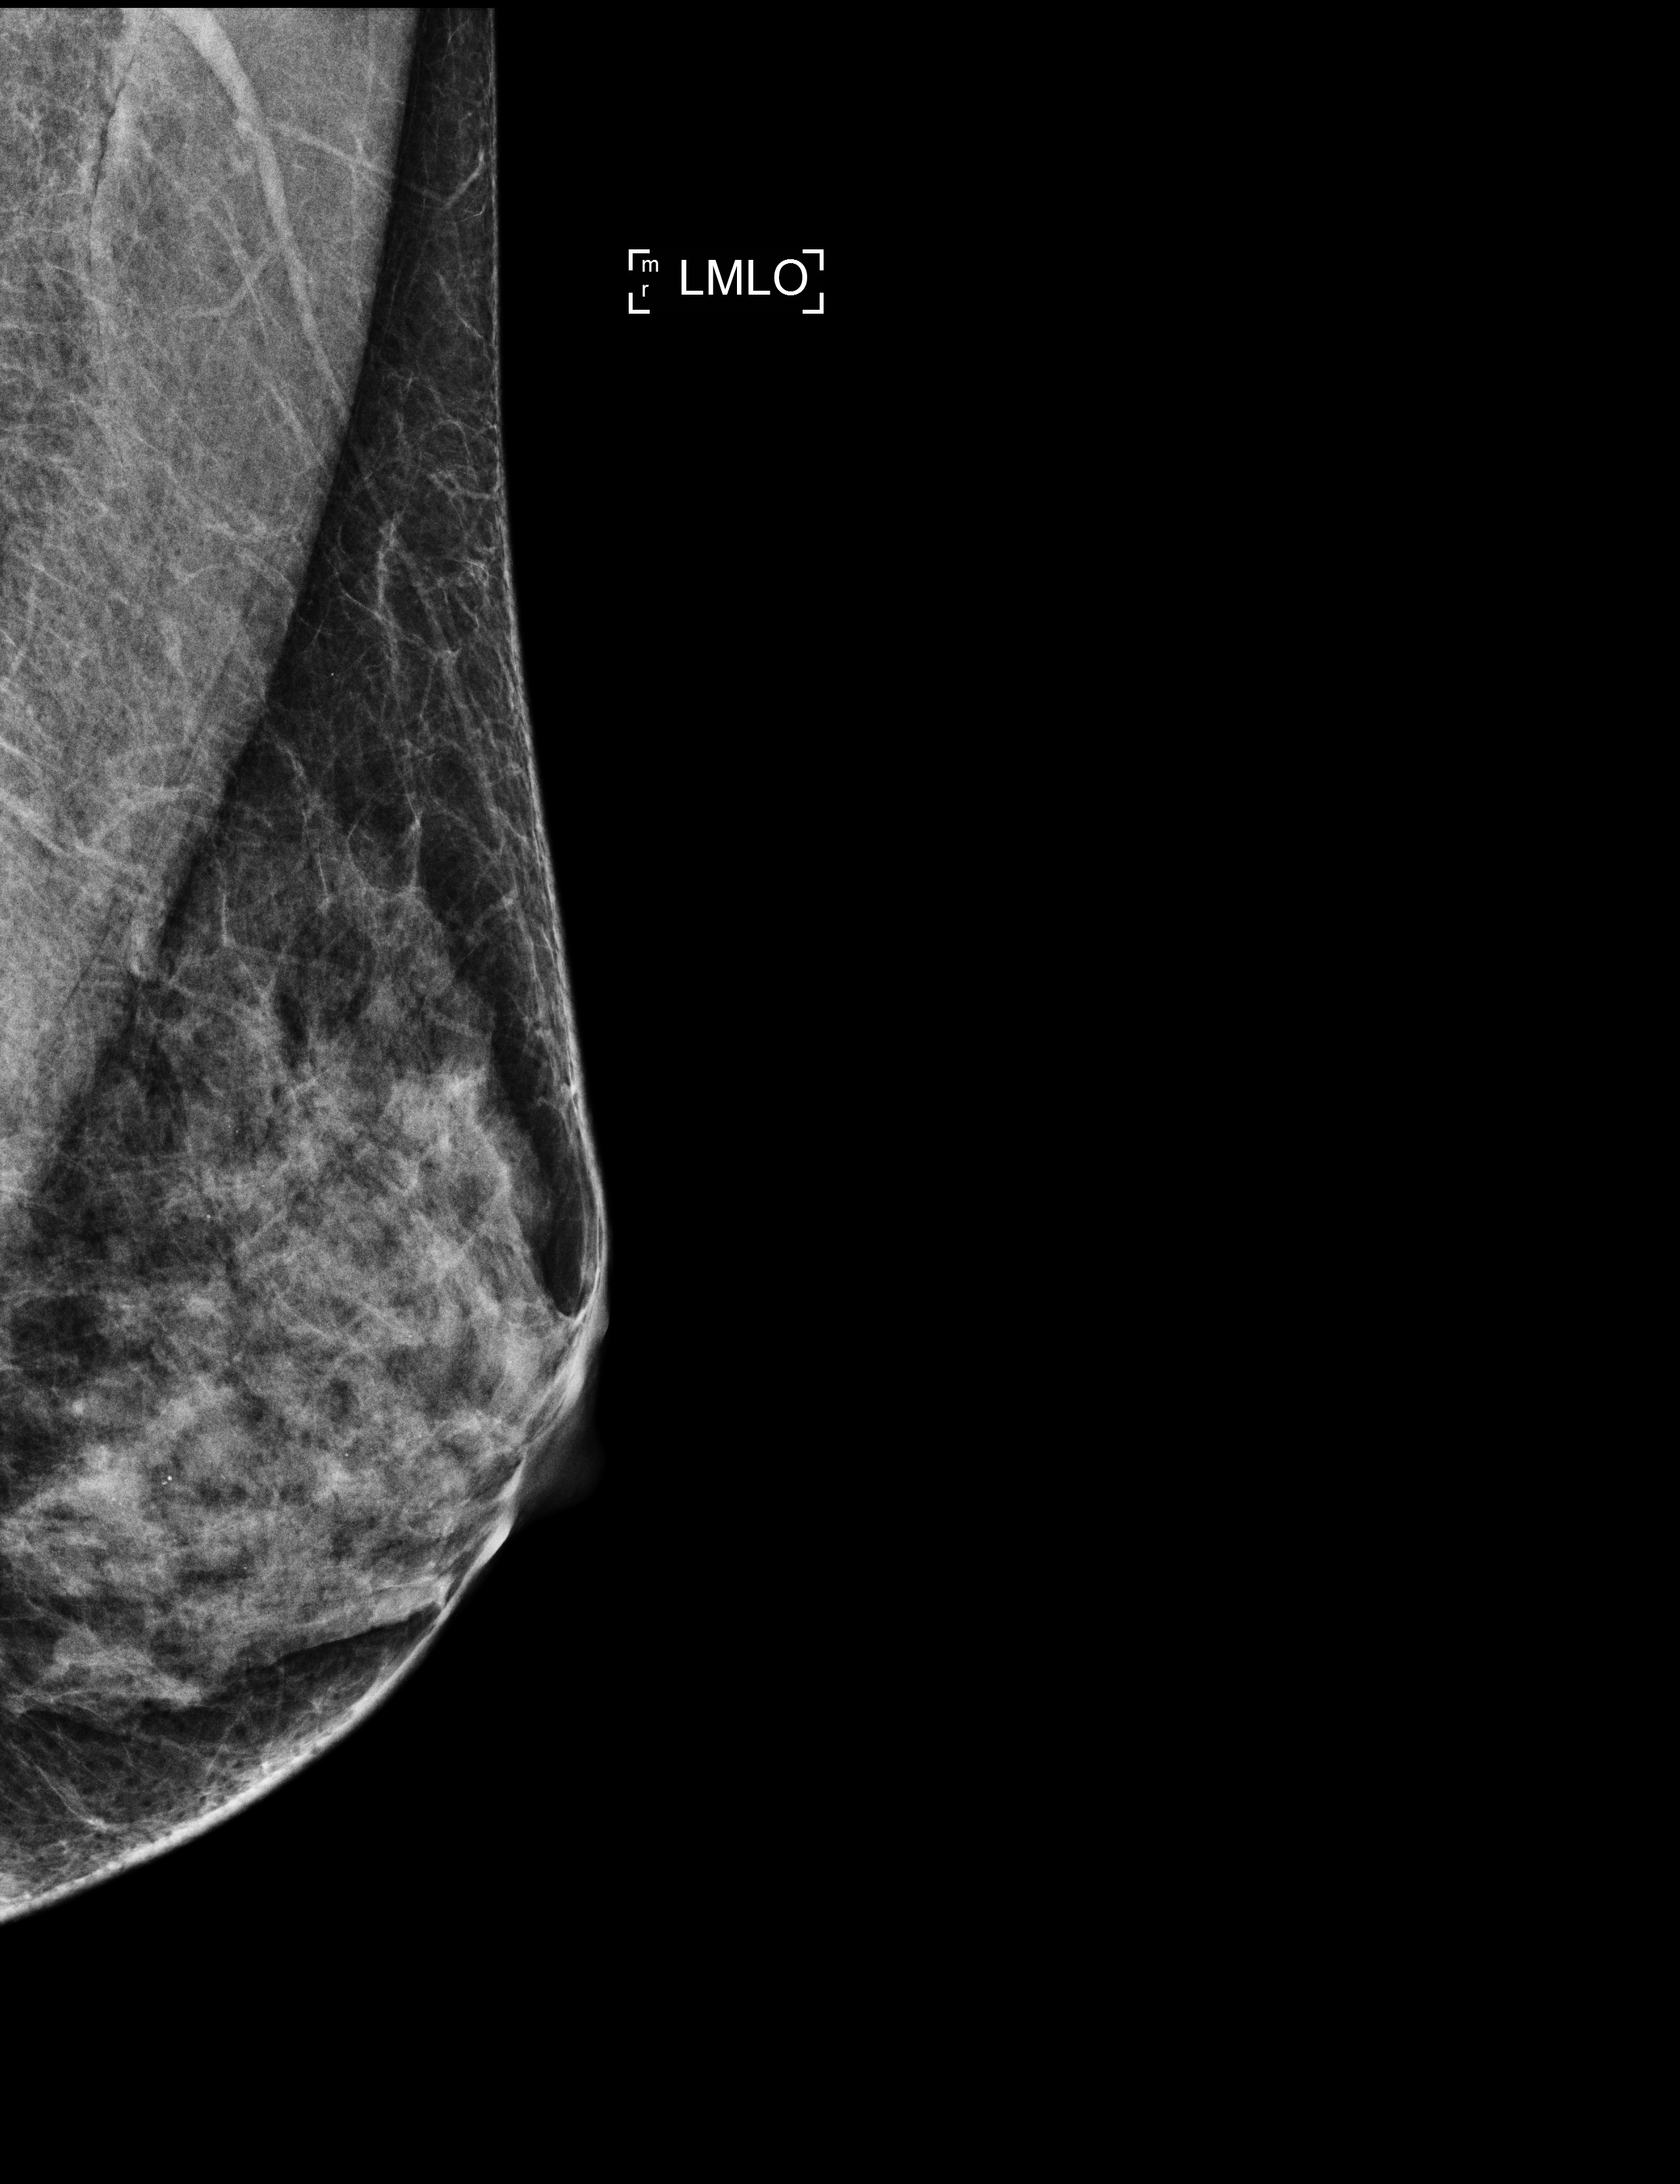
Annual screening mammography examination. Patient aged 50 years (female).
Image type: full-field digital mammogram. Breast: left. Projection: medio-lateral oblique projection.